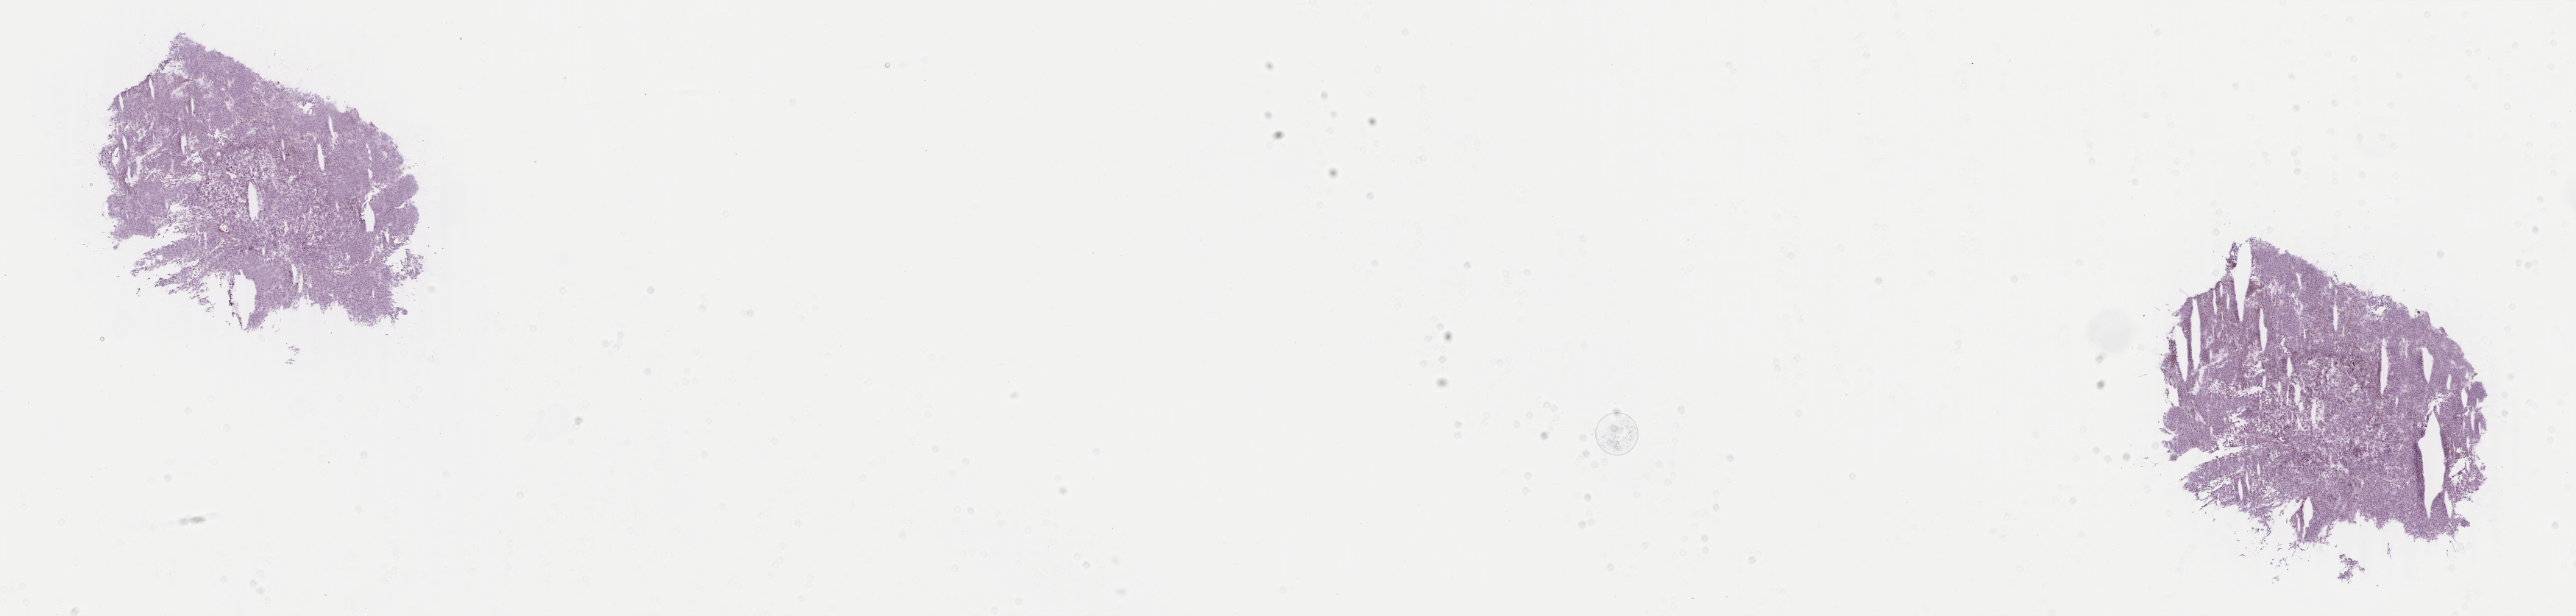
Digitized H&E tissue section (whole slide), a low-resolution overview of the entire scanned area, about 27.8 x 6.7 mm (from a 40x scan); frozen section from the top of the tissue portion; sample: primary tumour, uvea. Female, age 66 years at initial diagnosis. Slide review estimates, as recorded: tumour cells 100%, tumour nuclei 97%, normal cells 0%, stromal cells 0%, necrosis 0%. Infiltration values recorded for this section: lymphocyte infiltration 0%, monocyte infiltration 0%, neutrophil infiltration 0%.
TNM: T4a N0 M0. AJCC pathologic stage: IIIA. Pathologic diagnosis: Spindle cell melanoma, NOS (choroid). Laterality: right.